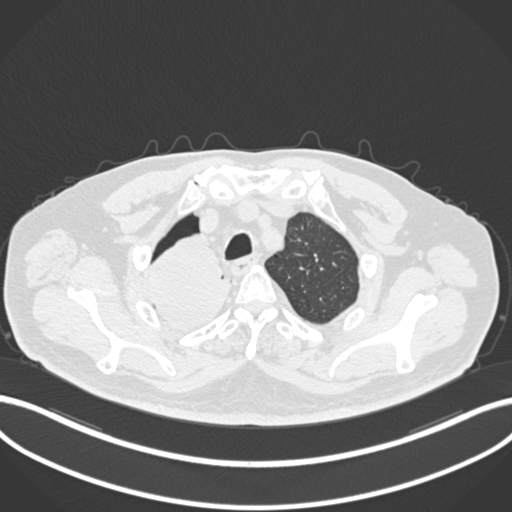
Chest CT, one axial slice; position 180 of 218 along the scan axis; reconstruction kernel B30f; 120 kVp; lung window (W 1500 / L -600 HU); 1 mm slice thickness; 512 × 512 image matrix. Male patient, age 68 years. Case-level facts recorded for this patient, not image findings: clinical TNM (as recorded): T2a N0 M0.
Outlined on this slice (bounding box drawn by a radiologist):
- lung tumour (recorded histology: adenocarcinoma): bounding box (x1, y1, x2, y2) in pixels: (138, 227, 232, 336)